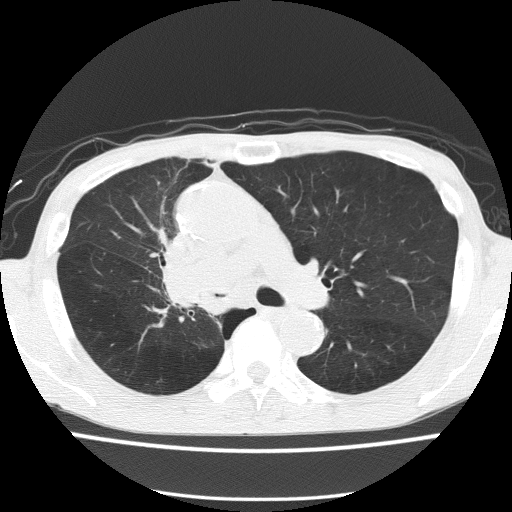
Low-dose screening chest CT, one axial slice. Reconstruction kernel FC51. Lung window (W 1500 / L -600 HU). 2 mm slice thickness. 512 × 512 image matrix, field of view 336 × 336 mm.
Outlined on this slice (outlined manually by an expert reader):
- lesion 1 (tumor, hilum of right lung): bounding box (x1, y1, x2, y2) in pixels: (165, 234, 228, 315)